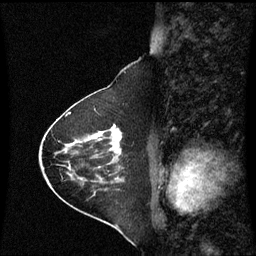
Breast MRI (dynamic contrast-enhanced), one sagittal slice. Position 27 of 60 along the scan axis. Dynamic contrast-enhanced series, image 2 of 3 at this slice position (ordered by acquisition). 1.5 T. TE 4.2 ms, TR 8.9 ms. 2 mm slice thickness. 256 × 256 image matrix. Patient: female, 63 years. Case-level facts recorded for this patient, not image findings: setting: breast cancer imaged before/during neoadjuvant chemotherapy; receptor status: HR-positive, HER2-negative.
Outlined on this slice (semi-automatically segmented with operator editing):
- analysis volume of interest (the breast-tissue region the enhancement analysis was run in; not a lesion): bounding box <88,125,123,163> (left, top, right, bottom; pixels)
- tumour enhancement mask (voxels above the 70 % enhancement threshold inside the analysis volume of interest): <111,126,122,154>